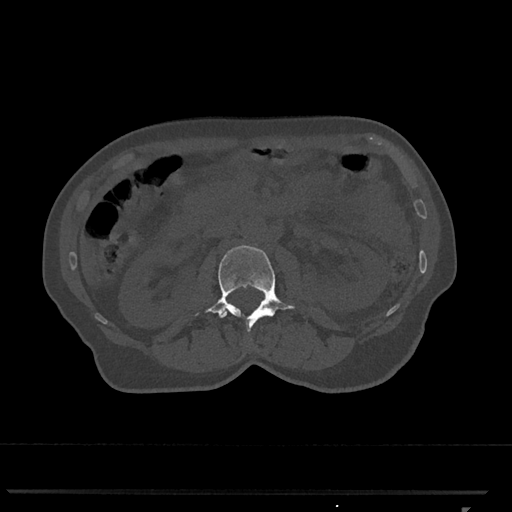
CT including the spine, one axial slice. Position 340 of 793 along the scan axis. 120 kVp. Bone window (W 1800 / L 400 HU). 0.5 mm slice thickness. 512 × 512 image matrix. Patient: female, 62 years. From the clinical record (not read from this slice): primary cancer: renal.
Outlined on this slice (semi-automatically segmented with operator editing):
- L2 vertebra: bounding box [x1, y1, x2, y2] px = [196, 245, 295, 332]